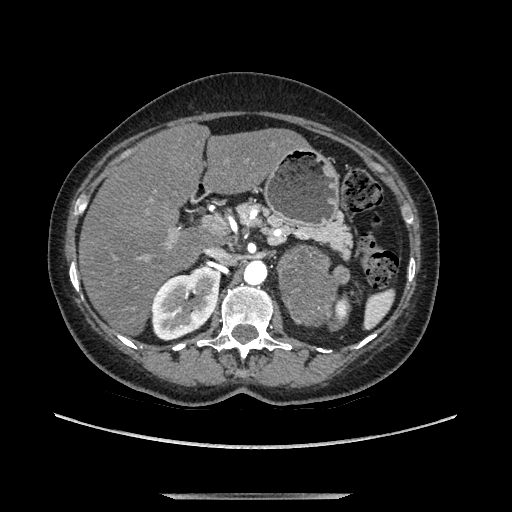
Contrast-enhanced abdominal CT, one axial slice. Position 71 of 169 along the scan axis. Soft-tissue window (W 400 / L 40 HU). 1.25 mm slice thickness. 512 × 512 image matrix, field of view 400 × 400 mm. Female patient. Case-level facts recorded for this patient, not image findings: diagnosis: adrenocortical carcinoma; tumour side: left adrenal; tumour size at pathology: 9 cm; Ki-67 index: 2 %; stage (as recorded): 3.
Structures marked on this image (semi-automatic segmentation, software-assisted and operator-edited):
- mass: bounding box [x1, y1, x2, y2] px = [282, 250, 348, 323]